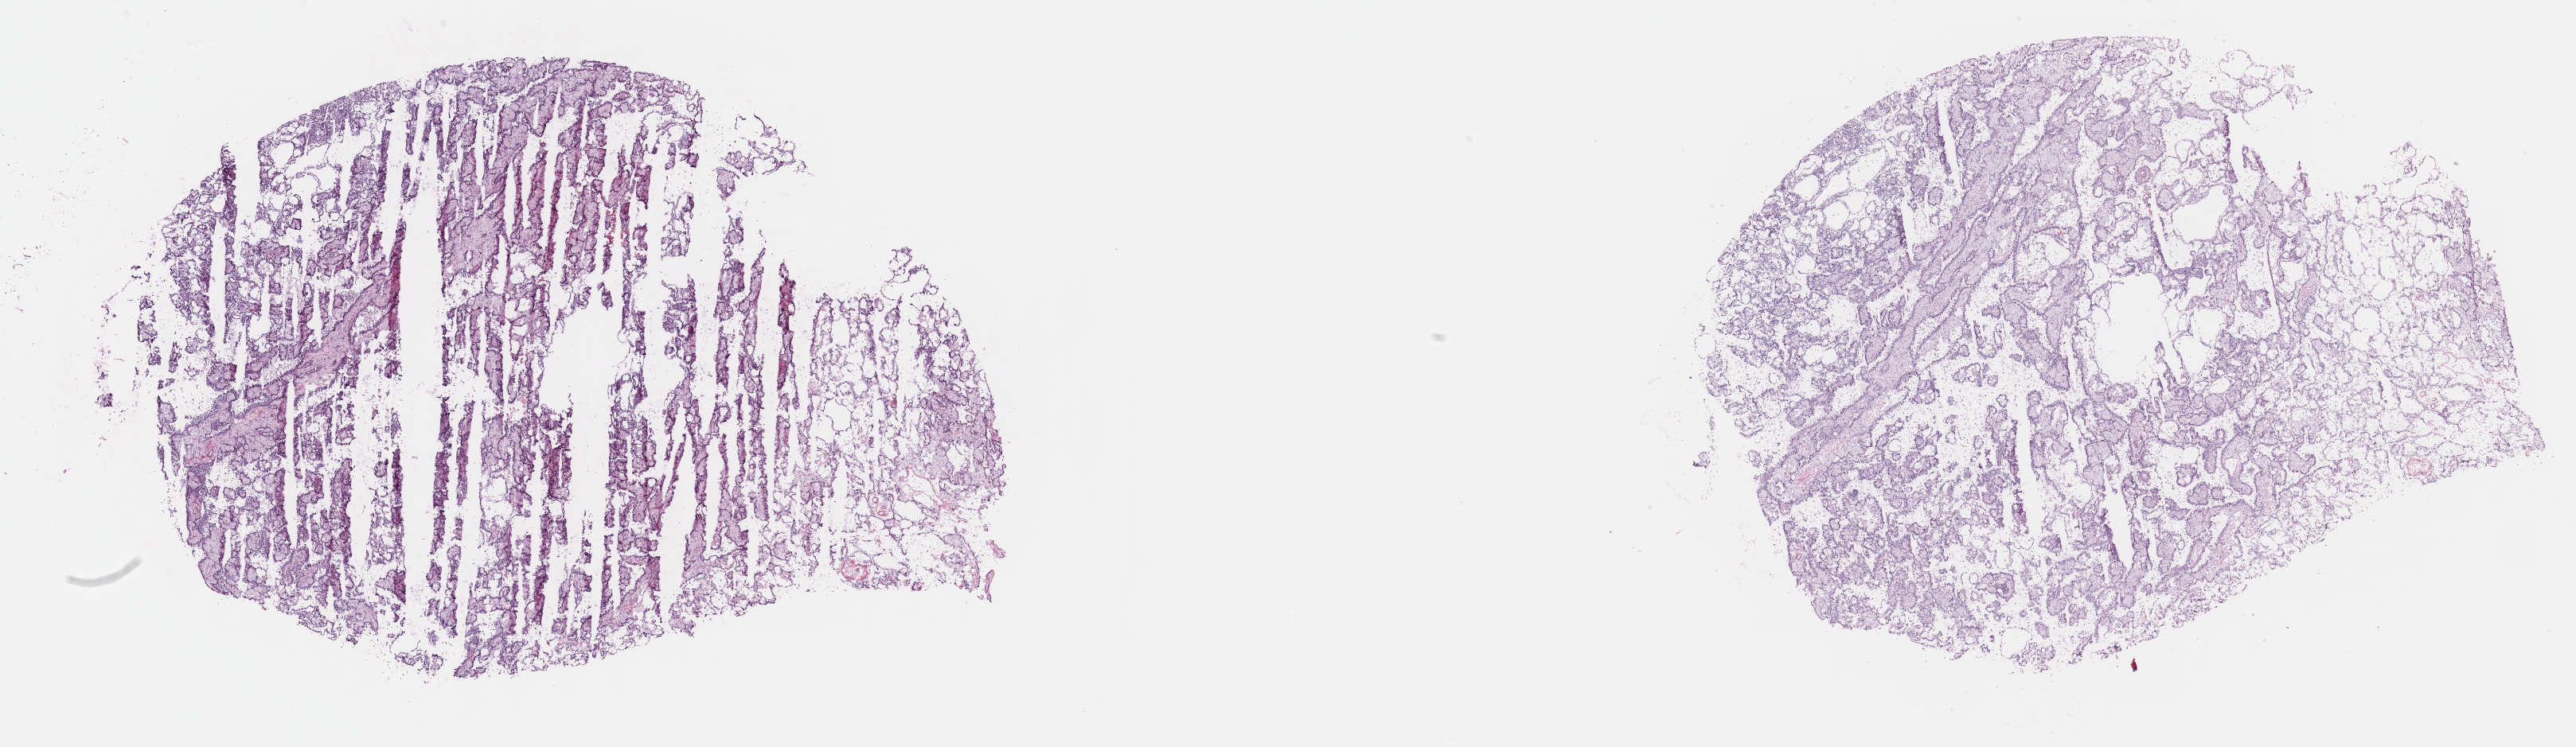
H&E whole-slide image, low-resolution overview of the scanned area, about 26.2 x 7.6 mm (slide scanned at 40x). Frozen section from the top of the tissue portion. Primary tumour sample from the kidney. Male, age 67 years at initial diagnosis. Composition of this section per pathologist review: tumour cells 40%, tumour nuclei 60%.
Histologic diagnosis: Papillary adenocarcinoma, NOS.